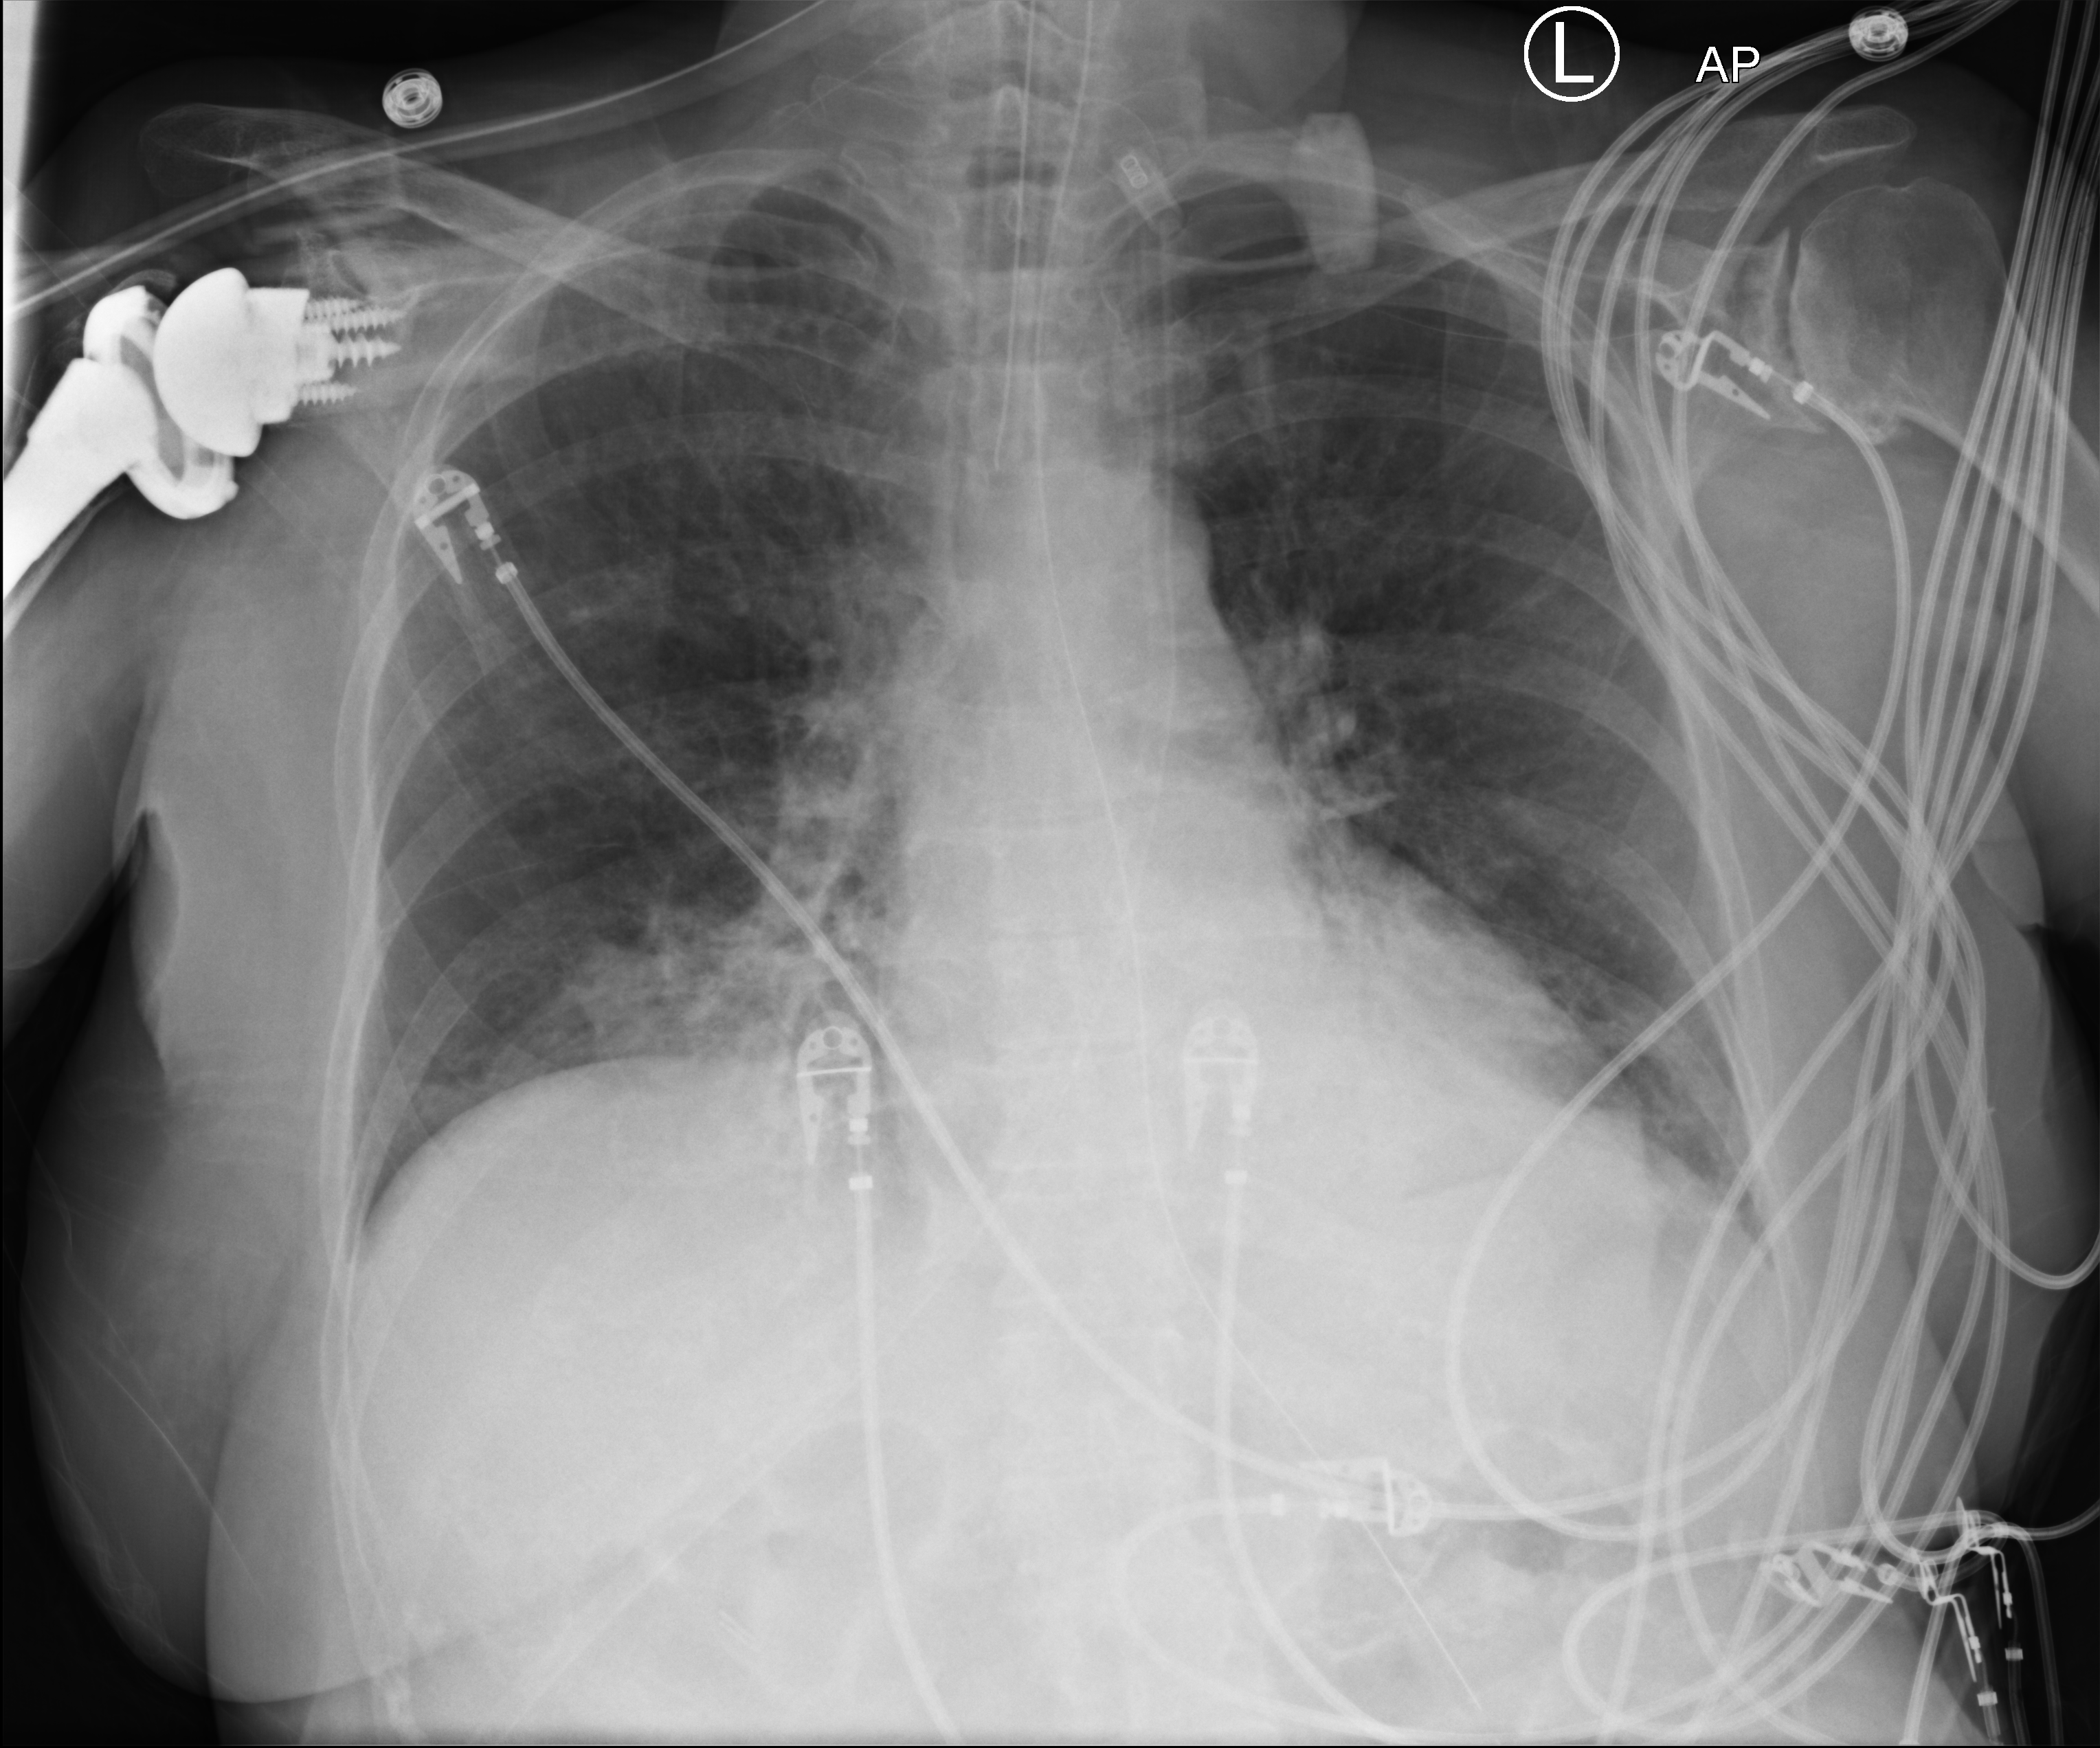
Chest X-ray (portable), anteroposterior (AP) projection. Female patient hospitalised with COVID-19, age 60–74 years.
Admission-level facts for this patient (not findings on this image; timing relative to this image not recorded):
- admitted to intensive care during this hospital stay: yes